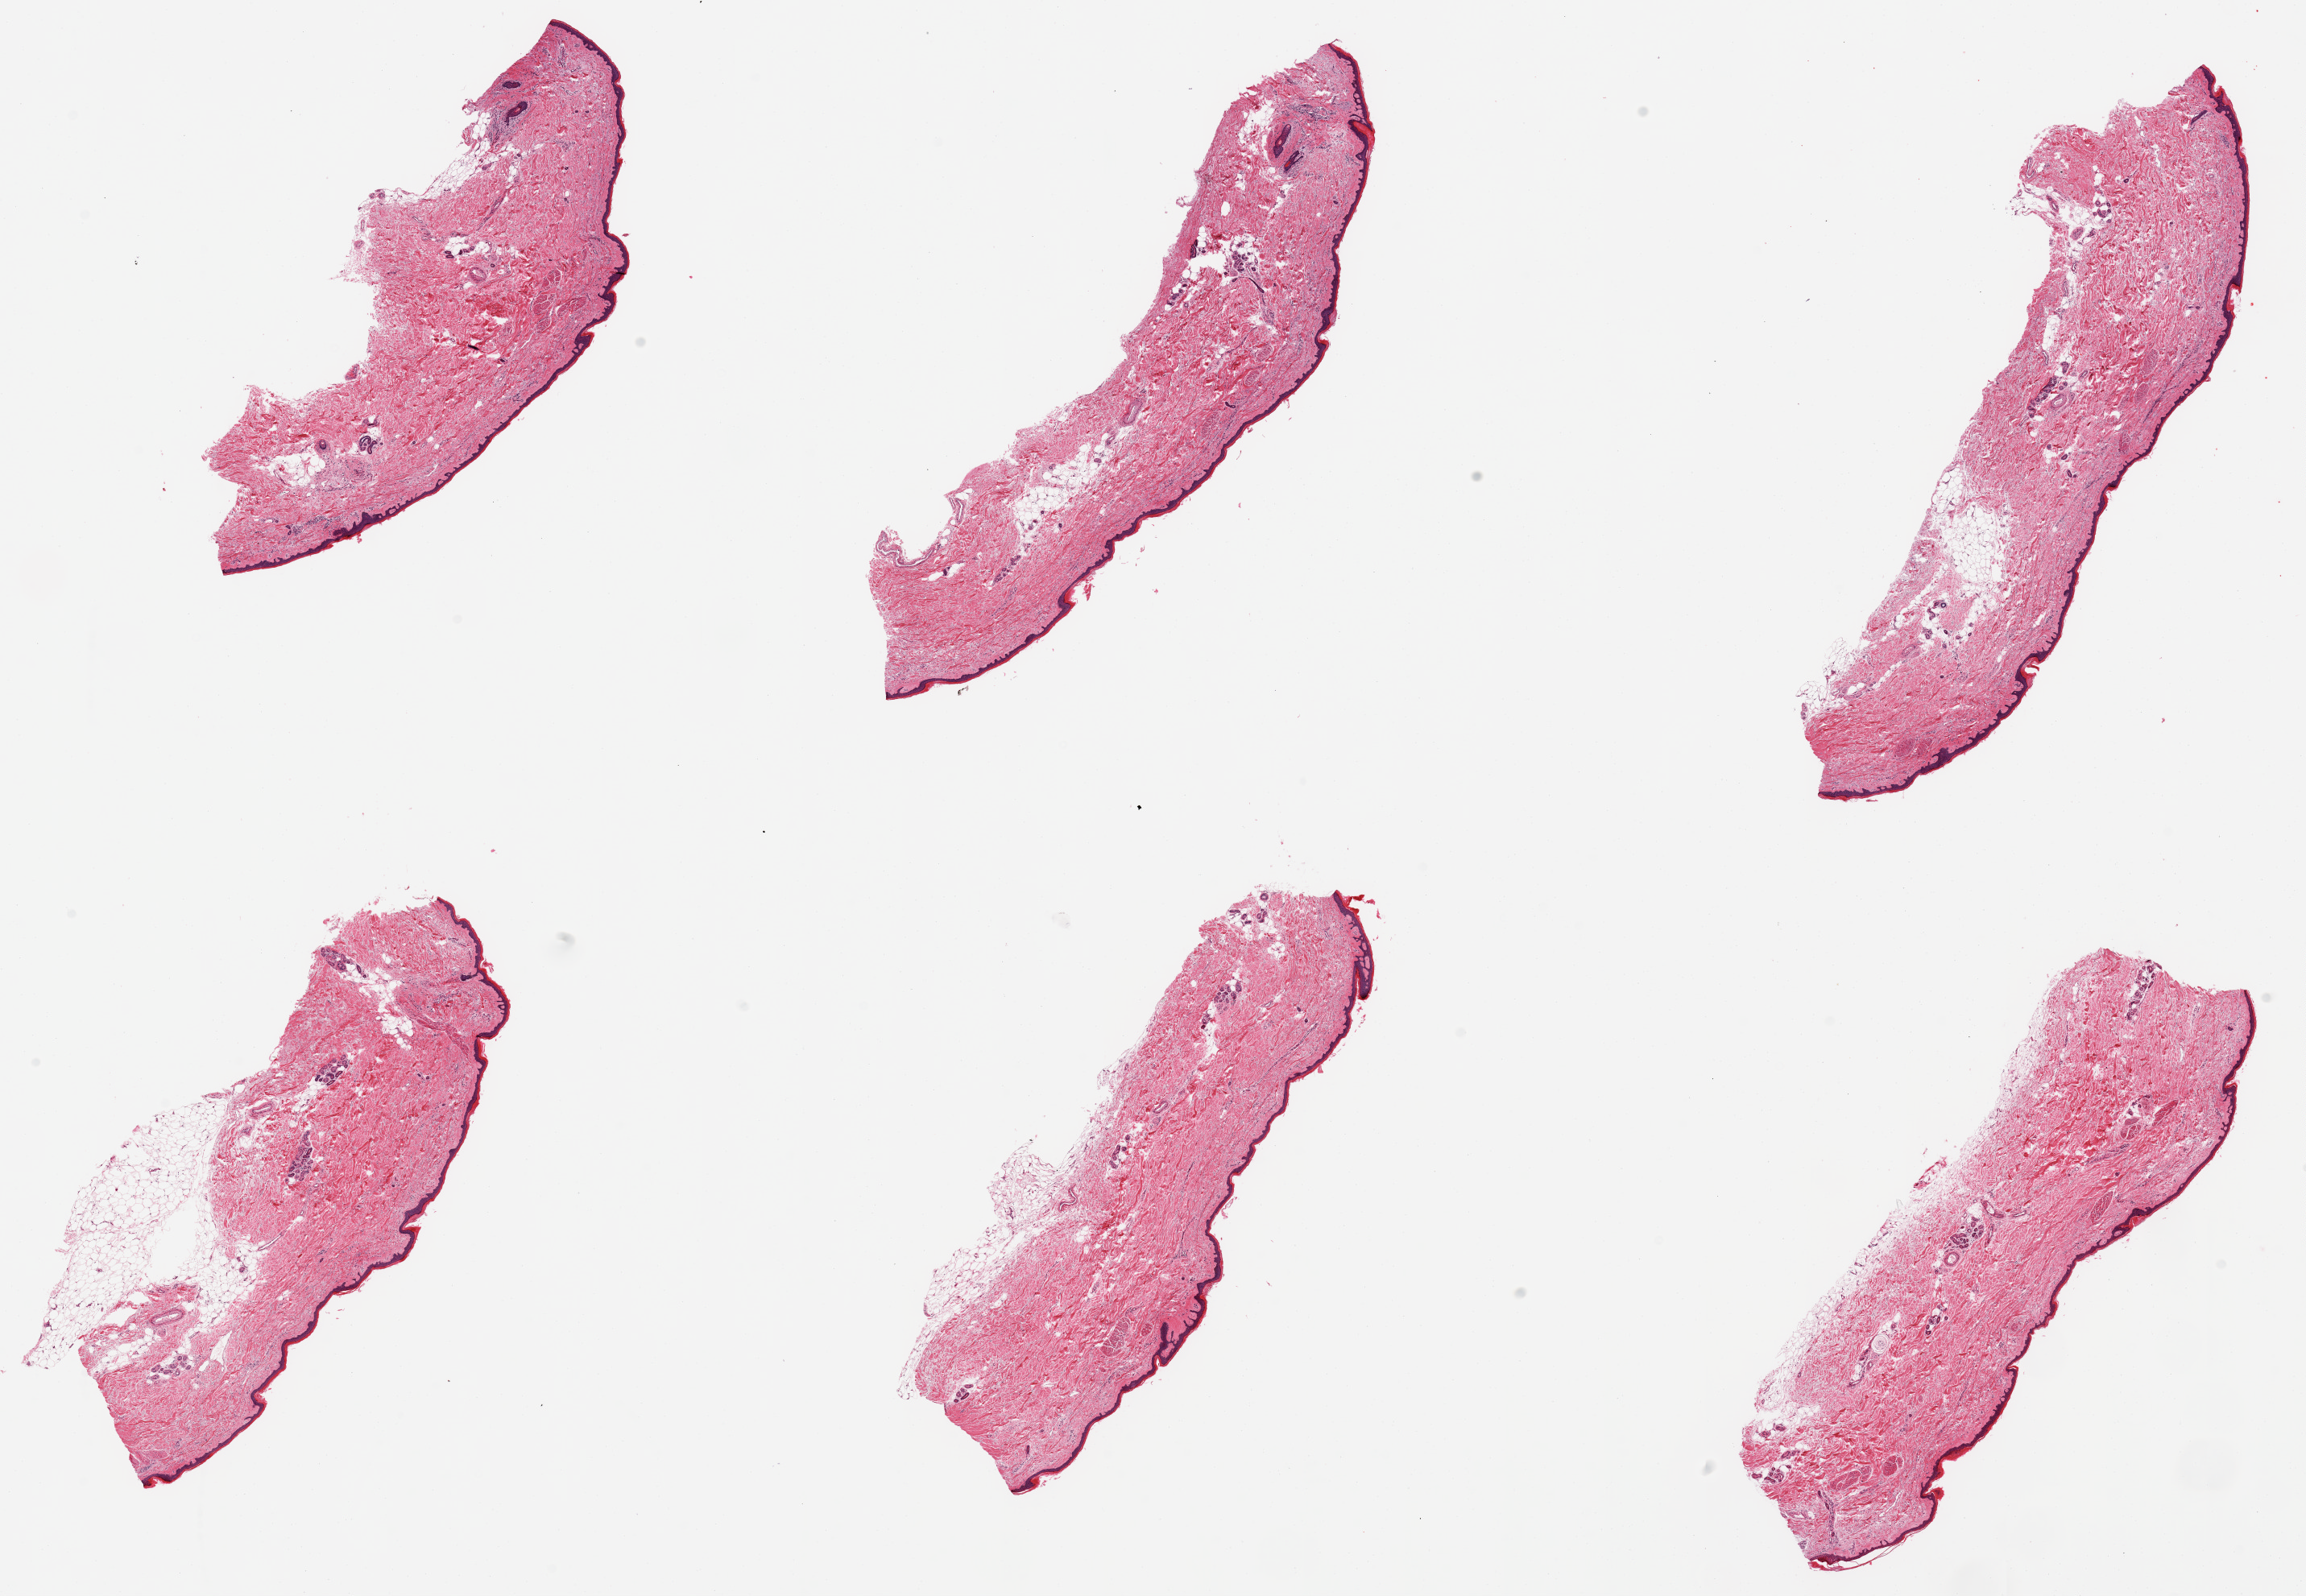
Whole-slide image, H&E stain, brightfield — low-resolution overview of the scanned area, about 22.6 x 15.7 mm, PAXgene-fixed, paraffin-embedded tissue, section of skin of lower leg (target tissue), donor tissue sample. Female donor.
- reviewer comment on this tissue sample: 6 pieces, trace dermal fat, squamous epithelium is 50-60 microns, moderate dermal solar elastosis